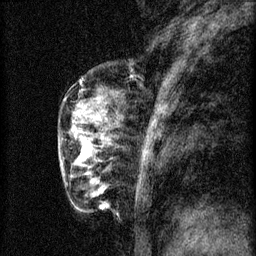
Breast MRI (dynamic contrast-enhanced), one sagittal slice; 3 images stored at this slice position (order not interpretable as contrast timing); 1.5 T; TE 4.2 ms, TR 8.2 ms; 256 × 256 image matrix. Female patient, age 56 years.
Outlined on this slice (semi-automatically segmented with operator editing):
- analysis volume of interest (the breast-tissue region the enhancement analysis was run in; not a lesion): bounding box [x1, y1, x2, y2] px = [60, 124, 114, 179]
- tumour enhancement mask (voxels above the 70 % enhancement threshold inside the analysis volume of interest): [83, 144, 91, 155]